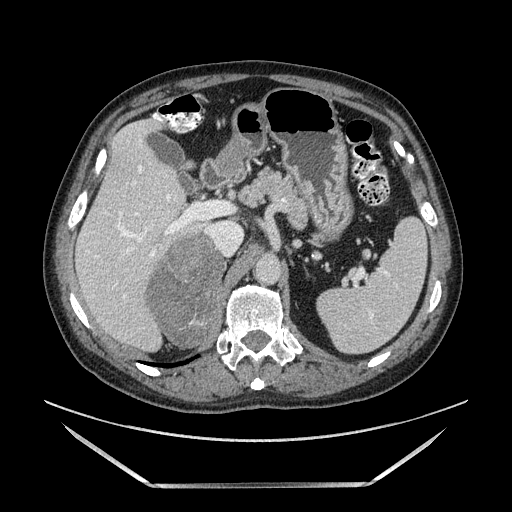
Contrast-enhanced abdominal CT, one axial slice. Slice 93 of 185 in the series (ordered by position). Soft-tissue window (W 400 / L 40 HU). 1.25 mm slice thickness. 512 × 512 image matrix, field of view 440 × 440 mm. Male patient. From the clinical record (not read from this slice): diagnosis: adrenocortical carcinoma; tumour side: right adrenal; tumour size at pathology: 10.3 cm; Ki-67 index: 20 %; stage (as recorded): 3.
Structures marked on this image (semi-automatically segmented with operator editing):
- mass: bounding box <148,232,226,348> (left, top, right, bottom; pixels)